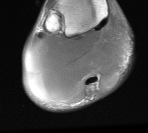
MRI of an extremity soft-tissue mass, one axial slice. Position 14 of 76 along the scan axis. MR volume resampled by the dataset authors to the PET/CT grid (not the native acquisition matrix). 148 × 133 image matrix. Male patient. From the clinical record (not read from this slice): histological type: liposarcoma - round cell; grade: high; site of the primary tumour: right calf.
Outlined on this slice (expert contour drawn on MRI and transferred to this co-registered scan by the dataset authors):
- gross tumour volume (mass): box from (x=26, y=21) to (x=128, y=104) px